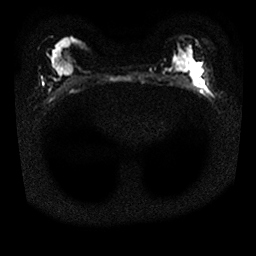
Breast MRI, one axial slice; position 16 of 25 along the scan axis; diffusion-weighted series; image 2 of 4 stored at this slice position (different b-values; order by instance number); 1.5 T; 4 mm slice thickness; 256 × 256 image matrix. Female patient.
Outlined on this slice (expert manual segmentation):
- tumour on diffusion-weighted imaging: bounding box <191,78,205,85> (left, top, right, bottom; pixels)